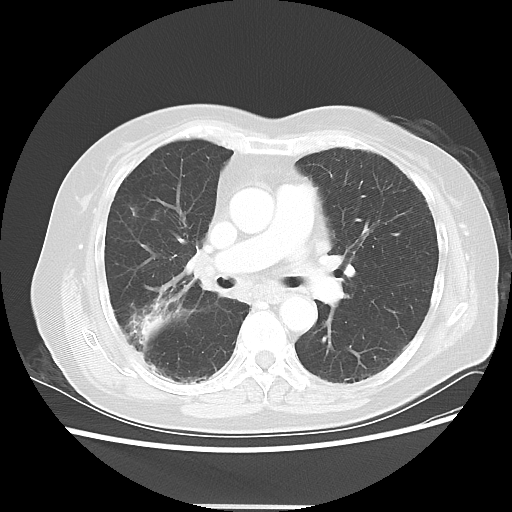
Chest CT, one axial slice; position 27 of 50 along the scan axis; reconstruction kernel LUNG; 120 kVp; lung window (W 1500 / L -600 HU); 5 mm slice thickness; 512 × 512 image matrix. Female patient, age 72 years. From the clinical record (not read from this slice): clinical TNM (as recorded): T2 N1 M0.
Structures marked on this image (bounding box drawn by a radiologist):
- lung tumour (recorded histology: adenocarcinoma): bounding box (x1, y1, x2, y2) in pixels: (136, 313, 174, 342)